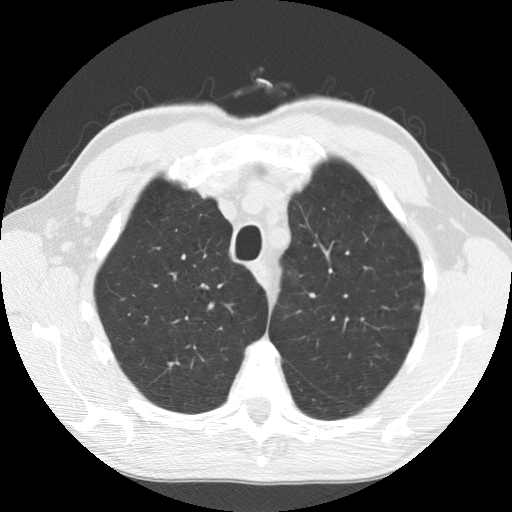
Axial slice from a low-dose chest CT screening exam, baseline annual screen, lung window (W 1500 / L -600 HU), 2.5 mm slice thickness, standard (soft-tissue) reconstruction kernel (STANDARD), 120 kVp, 512 × 512 image matrix. Male, age 63 years at enrolment. Current smoker at enrolment.
Expert reader's lesion annotation, bounding box <402,291,436,329> (left, top, right, bottom; pixels). No non-calcified nodule or mass ≥4 mm was recorded by the screening reader at this exam. Official screen result: negative screen, minor abnormalities not suspicious for lung cancer. Participant outcome: lung cancer diagnosed 858 days after this screen (after the third annual screen) — adenocarcinoma, NOS, left upper lobe, well differentiated (G1), stage IB (AJCC 6th edition), 5 mm at pathology.